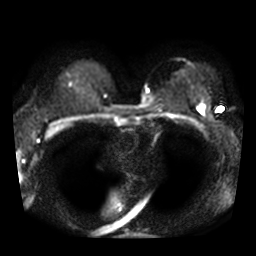
Breast MRI, one axial slice; slice 27 of 38 in the series (ordered by position); diffusion-weighted series; image 2 of 4 stored at this slice position (different b-values; order by instance number); 3 T; 256 × 256 image matrix, field of view 320 × 320 mm. Female patient.
Annotated regions visible in this slice (manually delineated by an expert):
- tumour on diffusion-weighted imaging: bounding box [x1, y1, x2, y2] px = [200, 106, 204, 114]